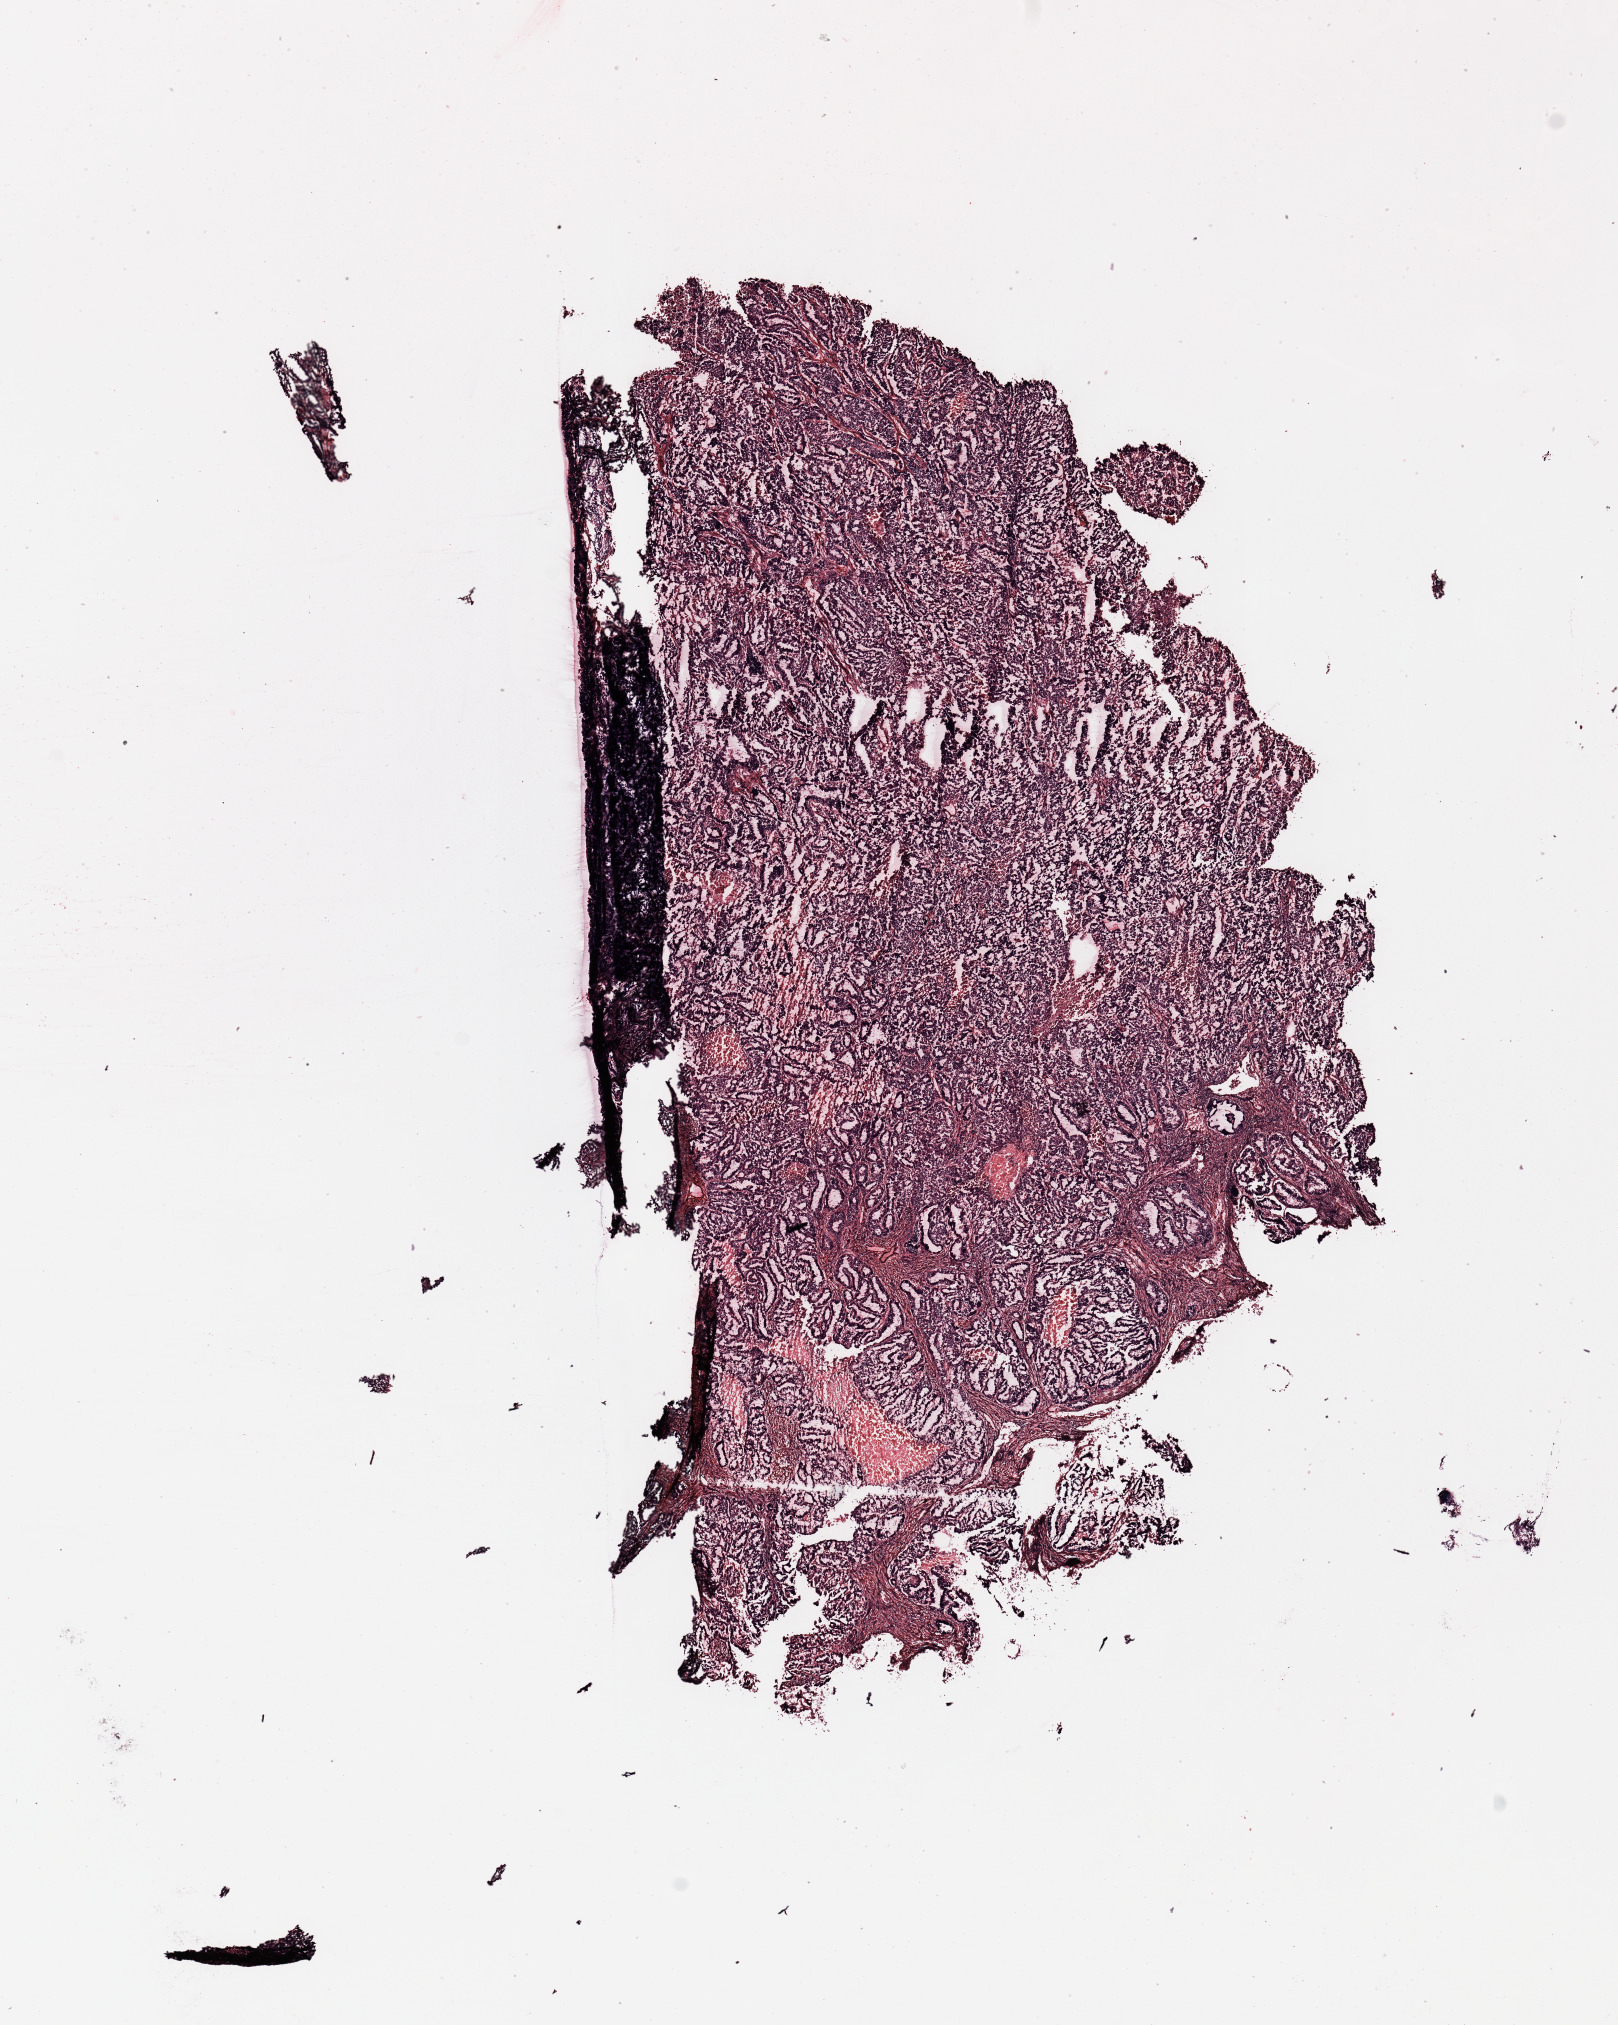
H&E whole-slide image, low-resolution overview of the scanned area, about 12.8 x 16.0 mm, uterus, tumour tissue. 78-year-old female patient. Histologic grade: G2 (moderately differentiated).
Diagnosis: Endometrioid adenocarcinoma, NOS. AJCC pathologic stage: I.